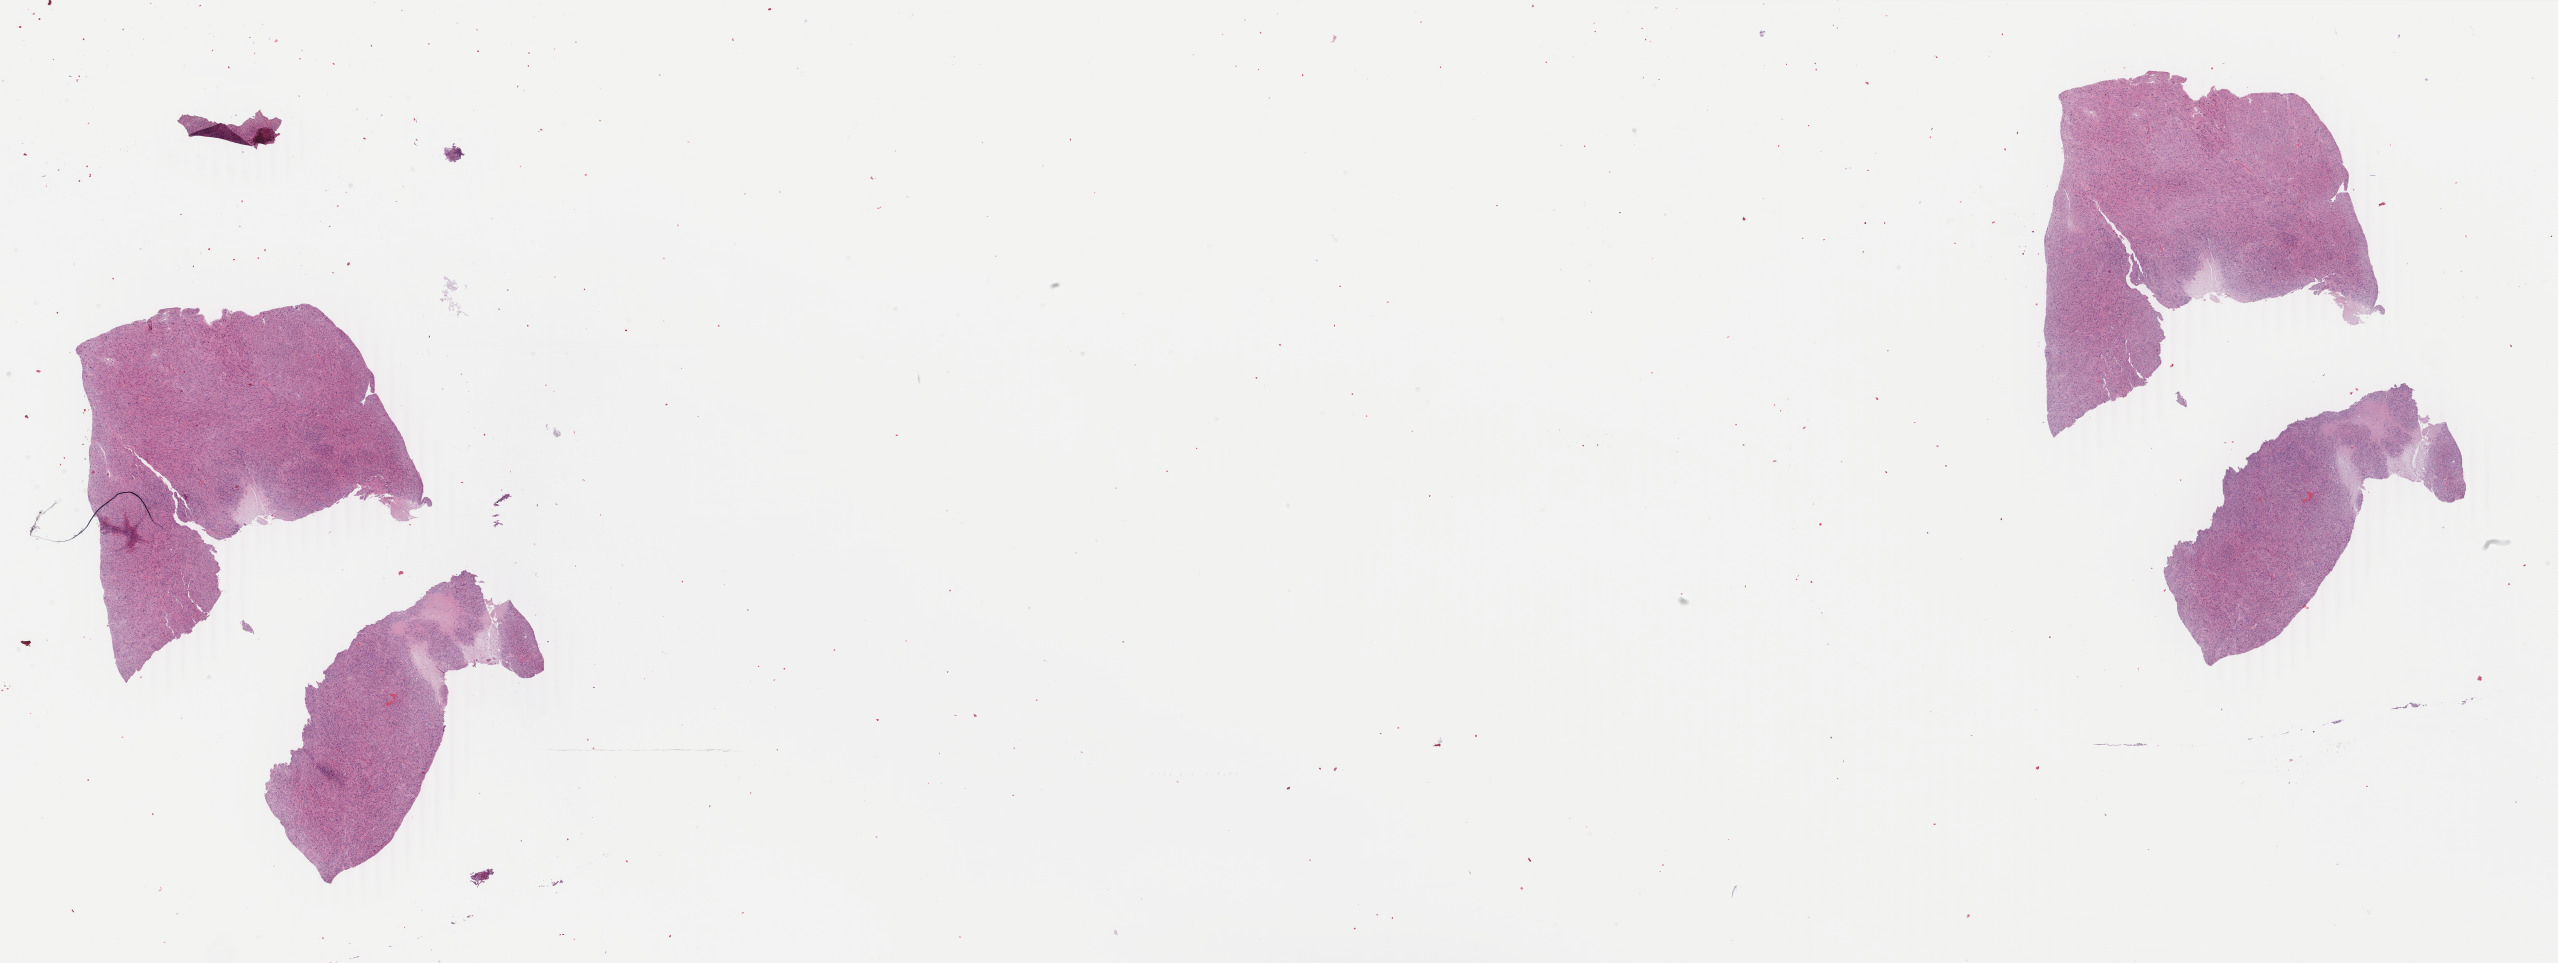
Whole-slide histology image, Hematoxylin and eosin (H&E) stained — low-resolution overview of the scanned area, about 40.7 x 15.3 mm (acquisition: 40x scan), formalin-fixed paraffin-embedded (FFPE) diagnostic section, sample: primary tumour, retroperitoneum and peritoneum. Male patient; age at initial diagnosis 54 years.
* histologic diagnosis: Leiomyosarcoma, NOS